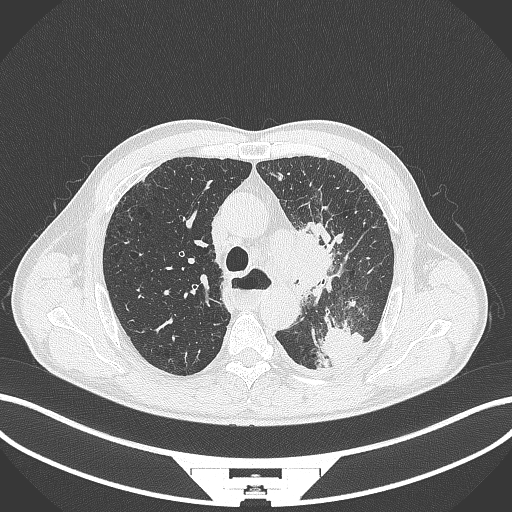
Chest CT, one axial slice. Slice 274 of 411 in the series (ordered by position). Reconstruction kernel B70f. 120 kVp. Lung window (W 1500 / L -600 HU). 1 mm slice thickness. 512 × 512 image matrix, field of view 400 × 400 mm. Patient: male, 57 years. From the clinical record (not read from this slice): clinical TNM (as recorded): T2a N1 M0.
Structures marked on this image (rectangle marked by the reading radiologist):
- lung tumour (recorded histology: squamous cell carcinoma): bounding box (x1, y1, x2, y2) in pixels: (292, 227, 335, 296)